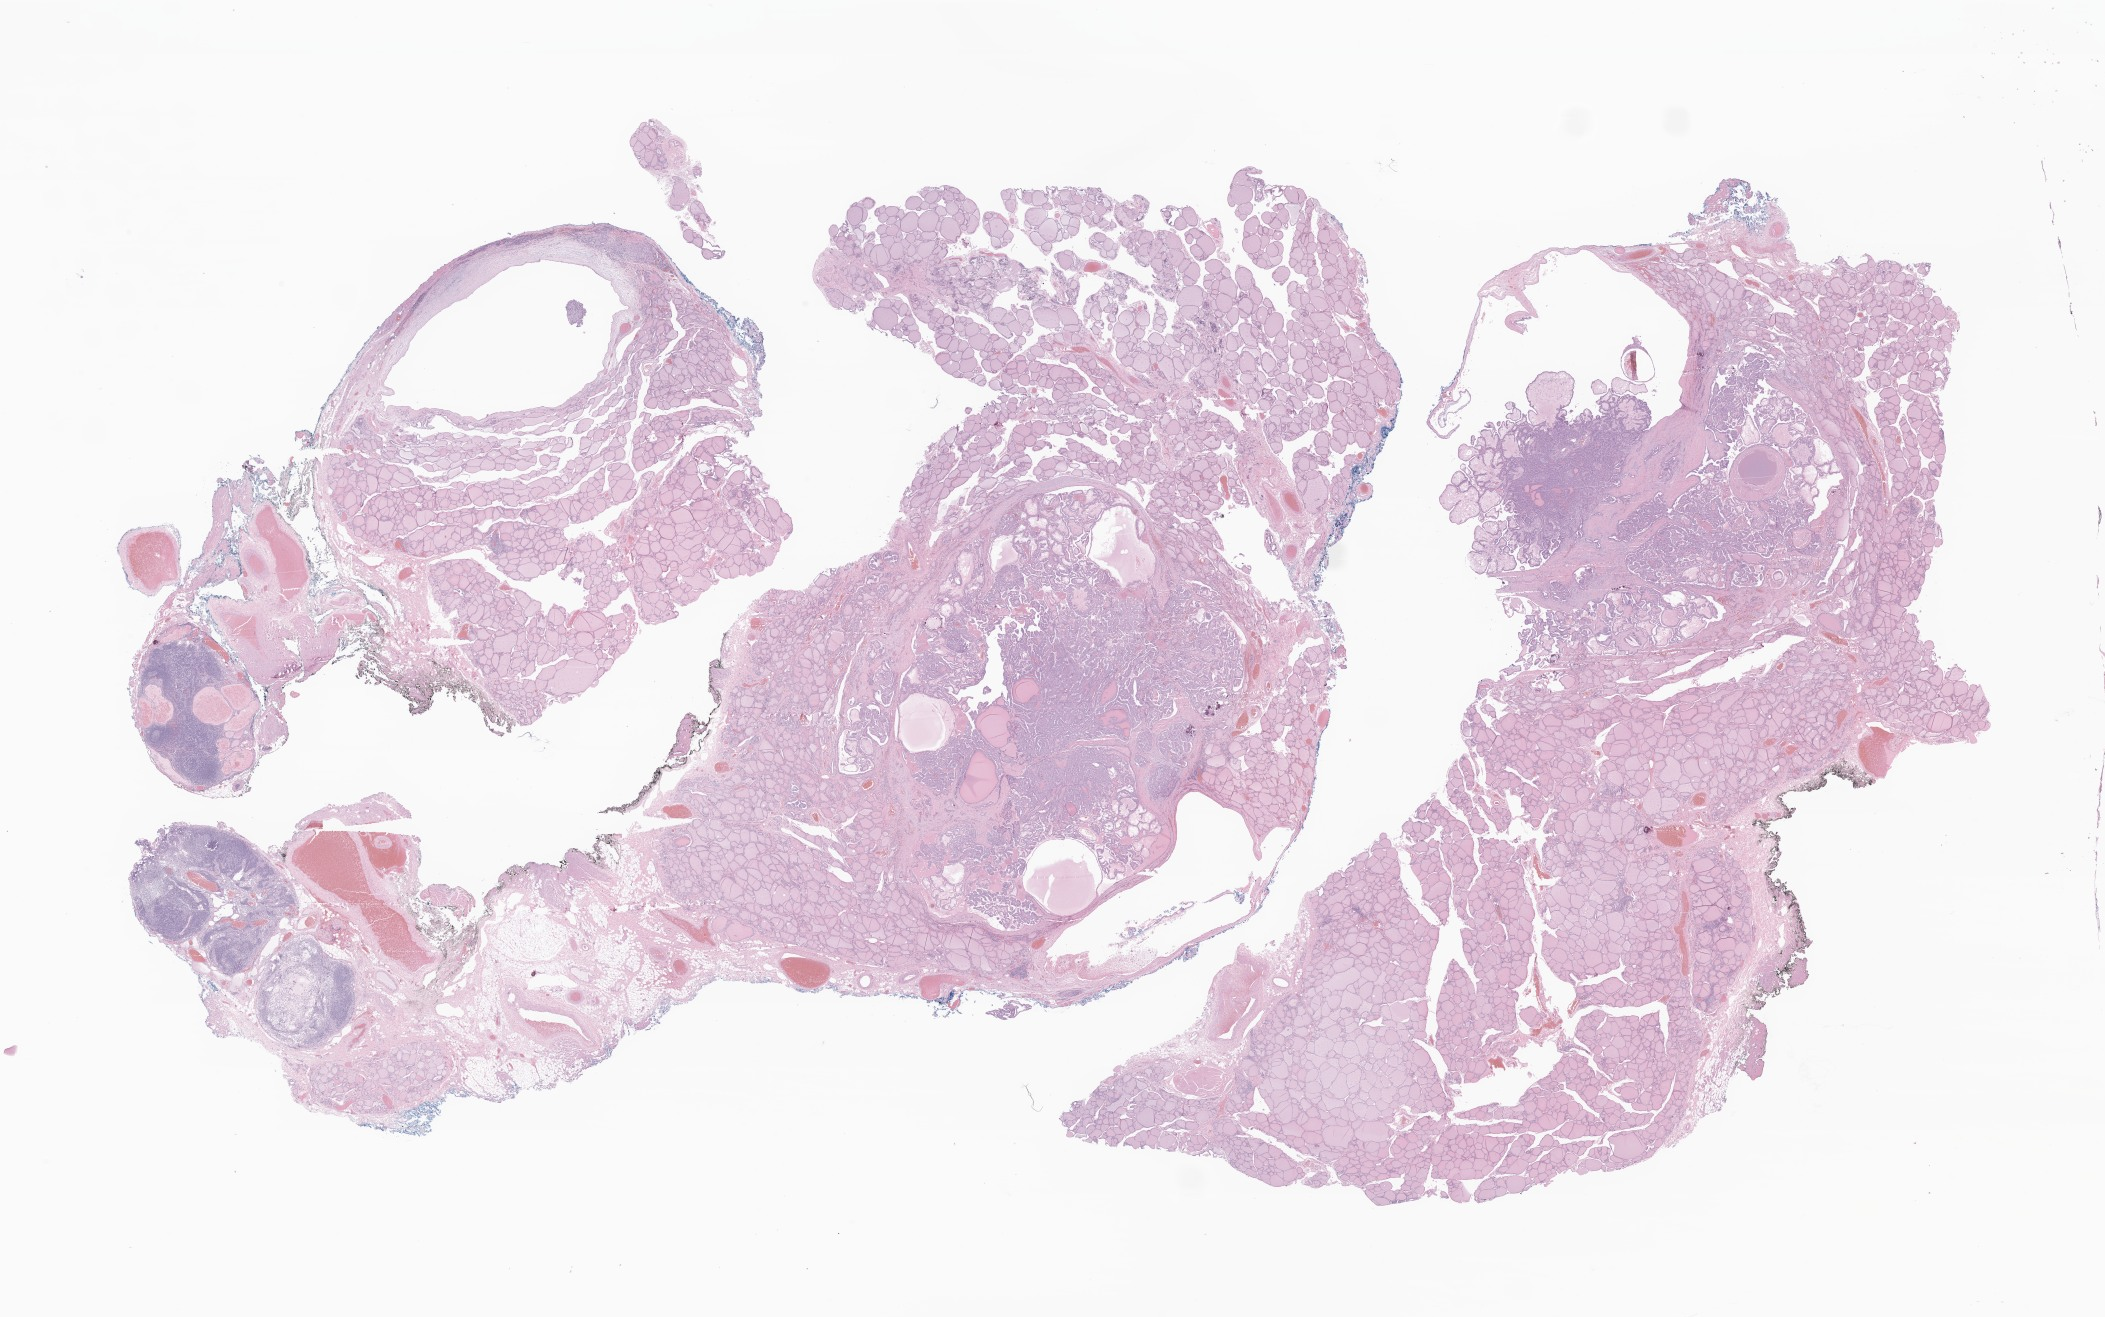
Hematoxylin and eosin (H&E) whole-slide image of tumor tissue from the thyroid — whole scanned area (about 35.5 x 22.2 mm) shown as a low-resolution overview; formalin-fixed, paraffin-embedded (FFPE) tissue. Female patient, age 214 months (17 years 10 months).
Diagnosis (ICD-O-3 morphology term): Papillary carcinoma, NOS.